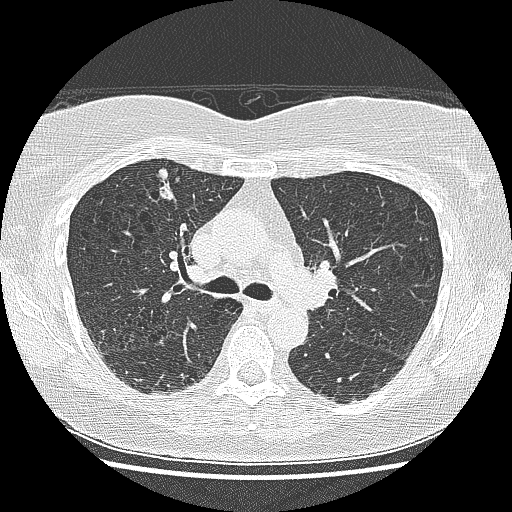
Low-dose screening chest CT, one axial slice; position 97 of 155 along the scan axis; reconstruction kernel LUNG; 120 kVp; lung window (W 1500 / L -600 HU); 2.5 mm slice thickness; 512 × 512 image matrix.
Annotated regions visible in this slice (manually delineated by an expert):
- lesion 1 (tumor, upper lobe of right lung): box from (x=153, y=168) to (x=176, y=202) px